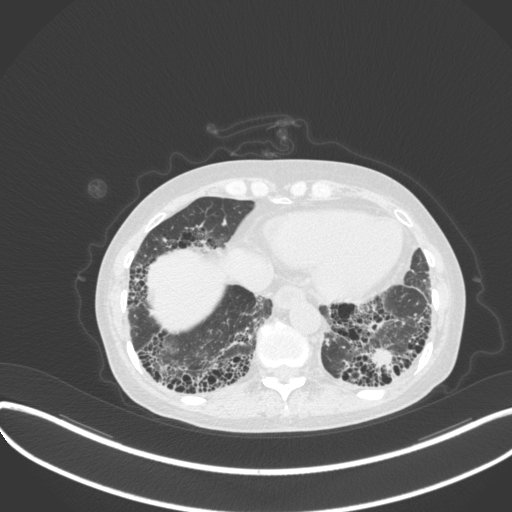
Chest CT, one axial slice; position 69 of 373 along the scan axis; reconstruction kernel B31f; lung window (W 1500 / L -600 HU); 1 mm slice thickness; 512 × 512 image matrix. Female patient, age 56 years. From the clinical record (not read from this slice): clinical TNM (as recorded): T1 N0 M0.
Outlined on this slice (bounding box drawn by a radiologist):
- lung tumour (recorded histology: adenocarcinoma): bounding box (x1, y1, x2, y2) in pixels: (368, 344, 401, 376)